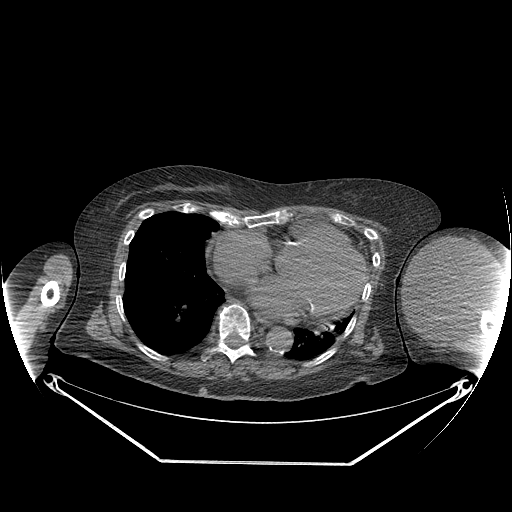
CT of an extremity soft-tissue mass (from a PET/CT study), one axial slice; slice 159 of 267 in the series (ordered by position); reconstruction kernel STANDARD; 140 kVp; soft-tissue window (W 400 / L 40 HU); 3.75 mm slice thickness; 512 × 512 image matrix. Female patient. From the clinical record (not read from this slice): histological type: pleiomorphic leiomyosarcoma; grade: high; site of the primary tumour: left biceps.
Annotated regions visible in this slice (expert contour drawn on MRI and transferred to this co-registered scan by the dataset authors):
- gross tumour volume including surrounding oedema: bounding box [x1, y1, x2, y2] px = [404, 235, 494, 330]
- gross tumour volume (mass): [404, 237, 494, 330]